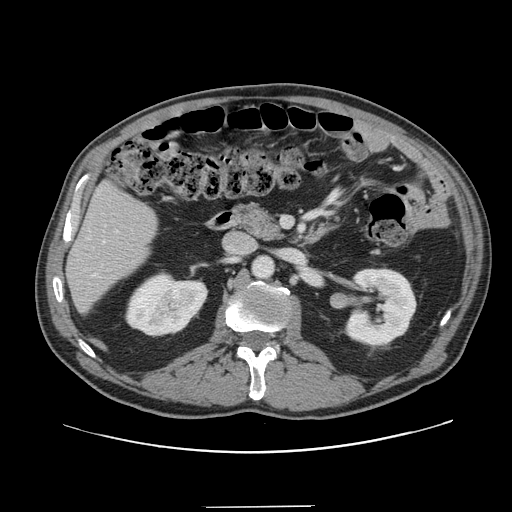
Contrast-enhanced abdominal CT, one axial slice. Position 64 of 139 along the scan axis. 120 kVp. Intravenous contrast given. Soft-tissue window (W 400 / L 40 HU). 512 × 512 image matrix, field of view 397 × 397 mm. Male patient, age 64 years. Case-level facts recorded for this patient, not image findings: diagnosis: colorectal cancer liver metastases, imaged before liver resection; multiple liver metastases: yes; largest metastasis: 3.5 cm; chemotherapy before resection: yes.
Outlined on this slice (expert manual segmentation):
- hepatic veins: bounding box [x1, y1, x2, y2] px = [103, 241, 105, 243]
- liver: [68, 185, 158, 311]
- planned liver remnant (the part of the liver to remain after resection): [68, 184, 158, 312]
- portal vein (with intrahepatic branches): [115, 230, 118, 233]